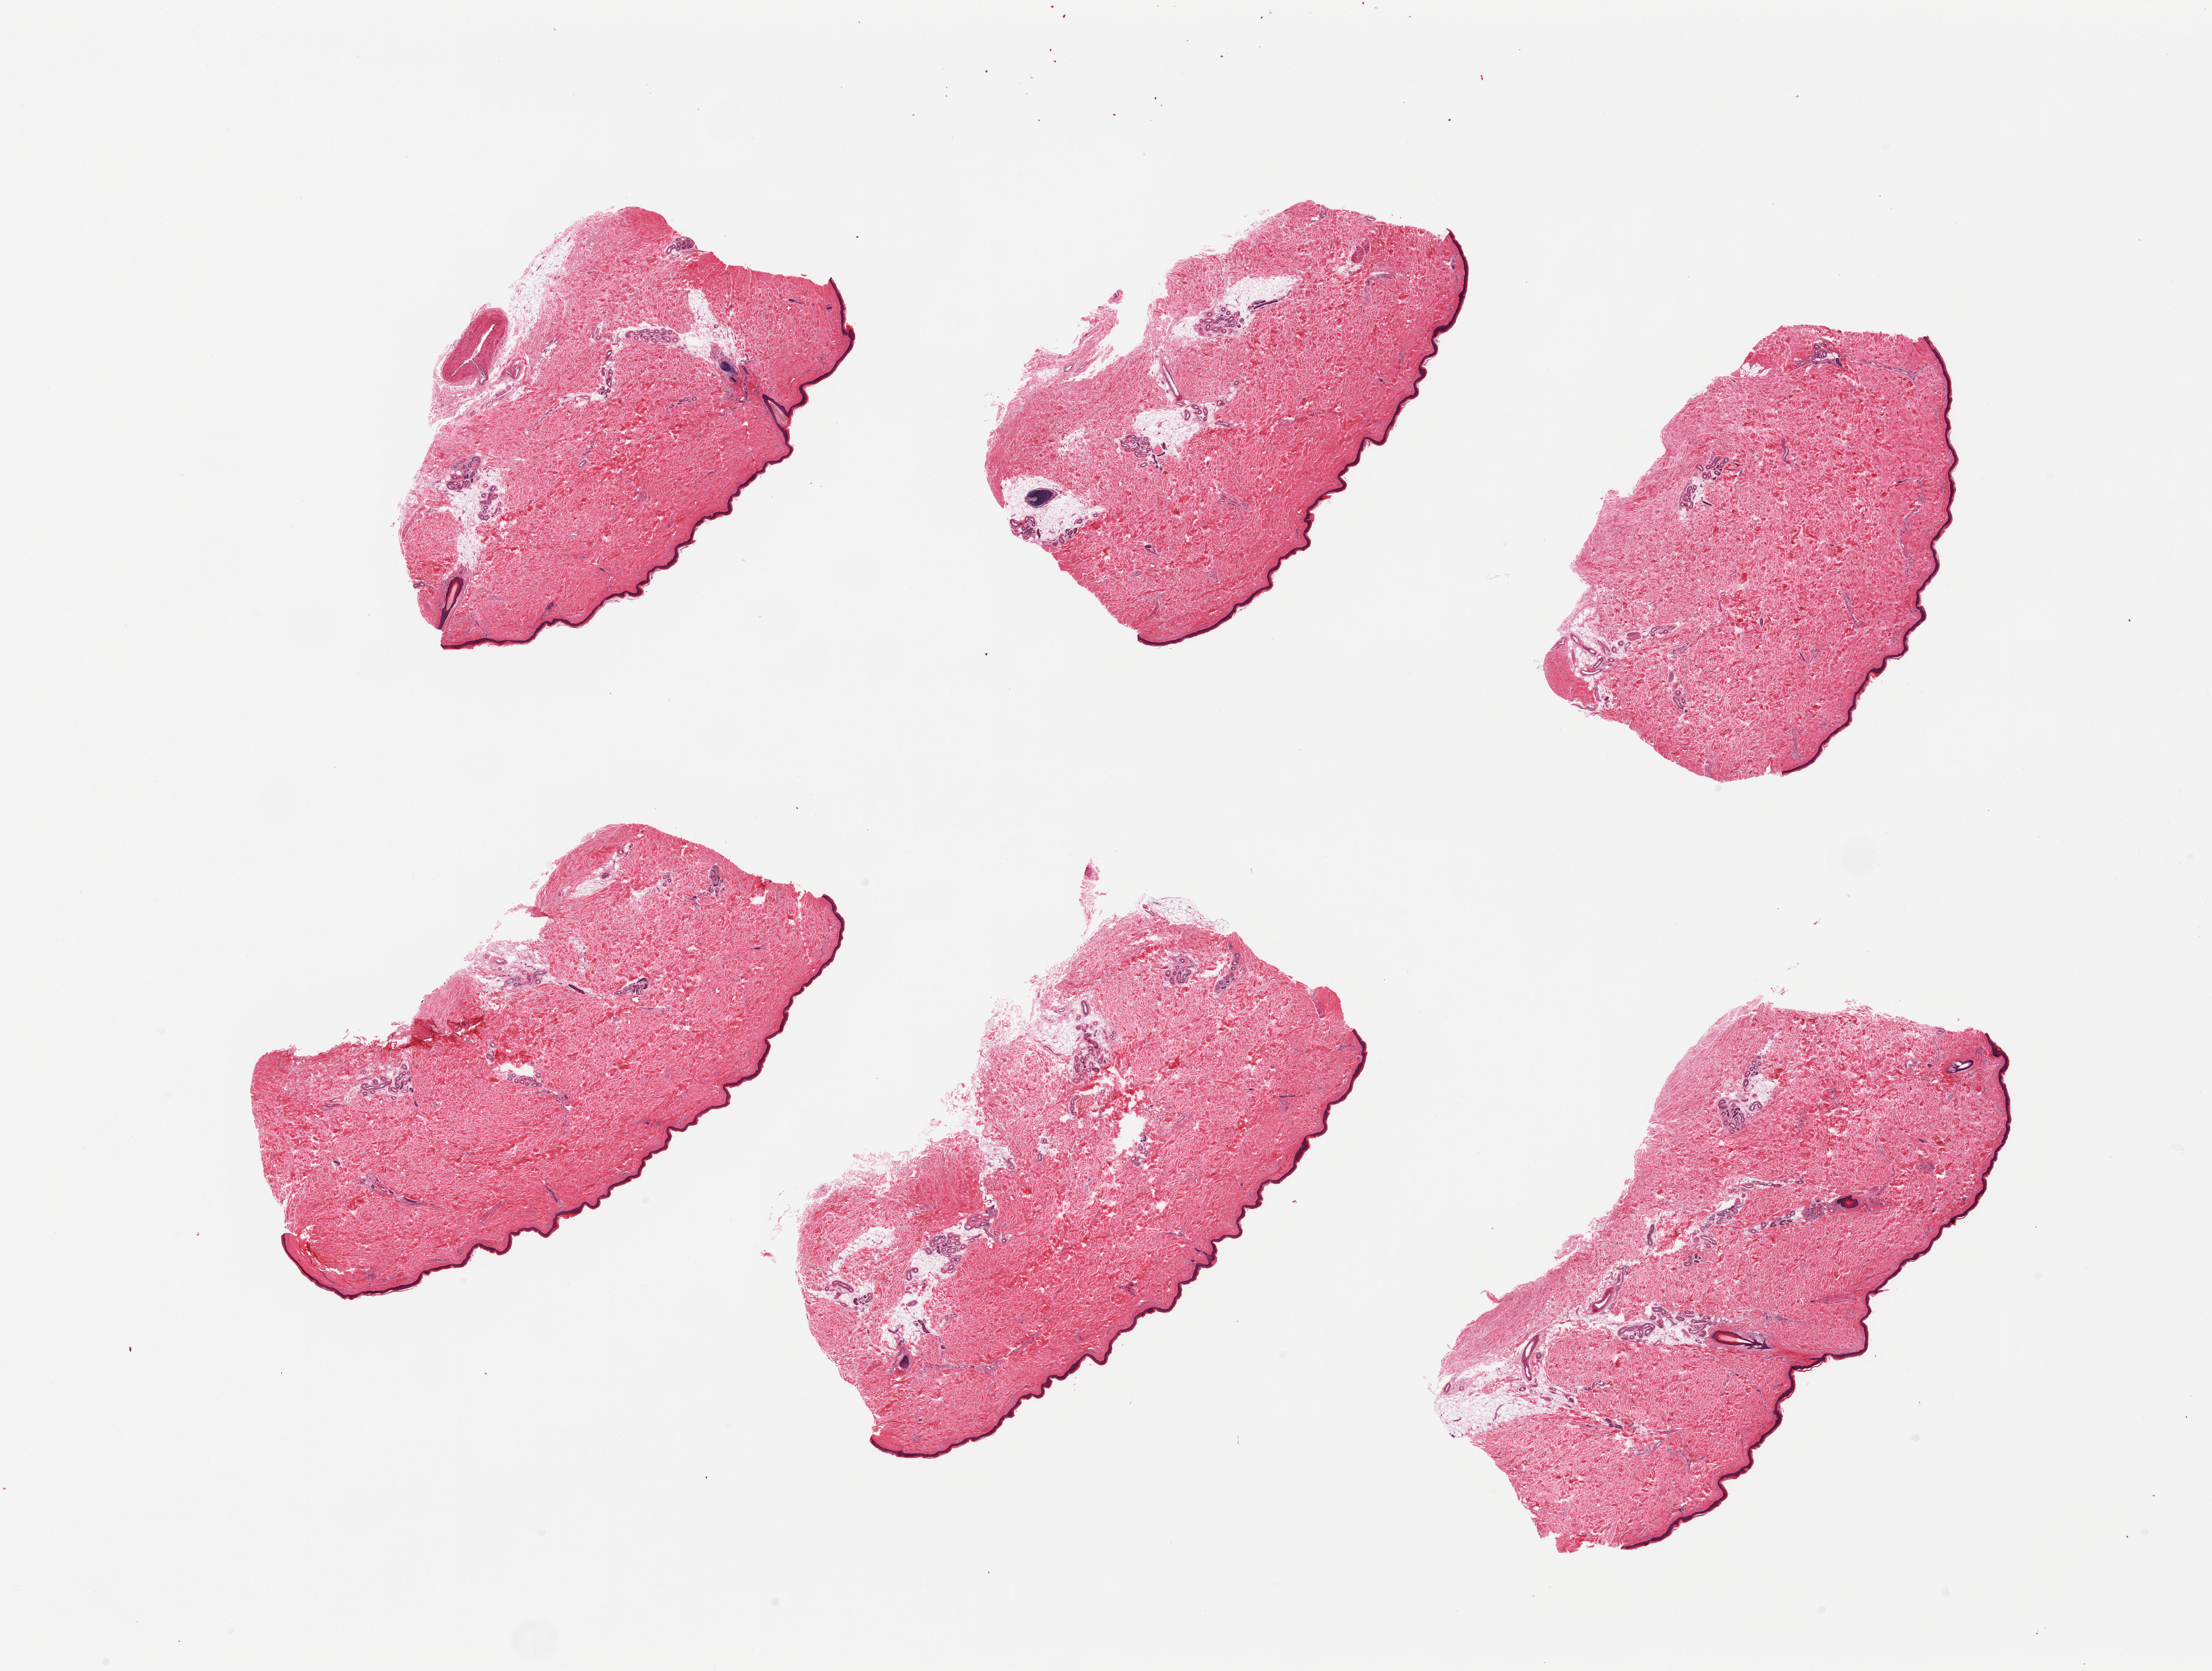
Digitized hematoxylin and eosin (H&E)-stained section, low-resolution overview of the scanned area, about 28.5 x 21.6 mm (from a 20x scan); PAXgene-fixed, paraffin-embedded tissue; sampled site (target tissue): skin of lower leg; donor tissue sample. Donor: male.
- review note (as recorded): 6 pieces; mostly periadnexal fat; ~36microns thick epidermis